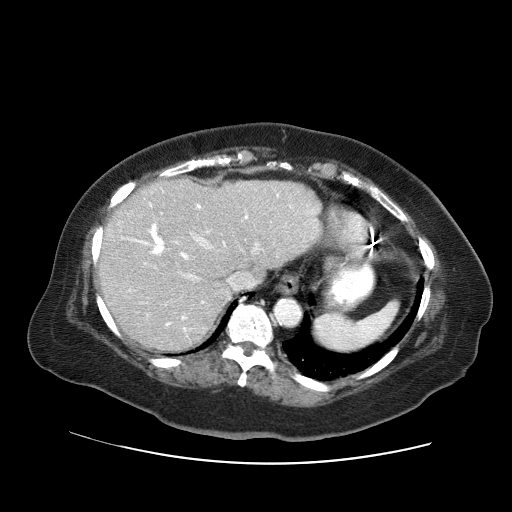
Contrast-enhanced abdominal CT (liver protocol), one axial slice. Slice 47 of 71 in the series (ordered by position). Soft-tissue window (W 400 / L 40 HU). 2.5 mm slice thickness. 512 × 512 image matrix, field of view 400 × 400 mm. From the clinical record (not read from this slice): diagnosis: hepatocellular carcinoma (patient treated with transarterial chemoembolisation; whether this scan precedes or follows treatment is not stated here); TNM stage (as recorded): Stage-II; Child-Pugh class: A; tumour differentiation: poorly differentiated; tumour size: 5 cm.
Outlined on this slice (semi-automatic segmentation, software-assisted and operator-edited):
- liver parenchyma outside the tumour (the mass and vessels are separate outlines, so this box may not span the whole liver): bounding box (x1, y1, x2, y2) in pixels: (98, 178, 322, 351)
- liver vessels: (122, 189, 315, 332)